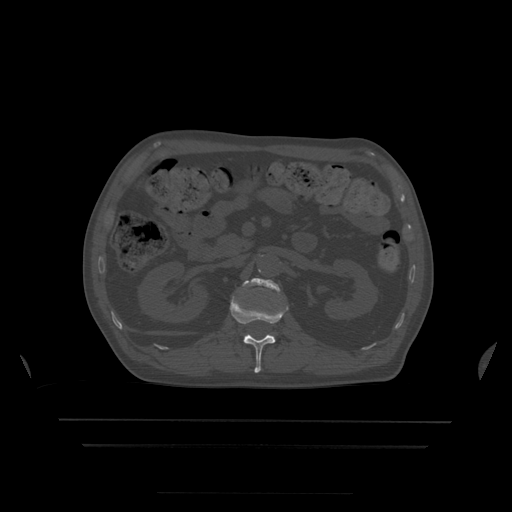
CT including the spine, one axial slice; position 164 of 522 along the scan axis; bone window (W 1800 / L 400 HU); 1.25 mm slice thickness; 512 × 512 image matrix, field of view 436 × 436 mm. Patient age 68 years. From the clinical record (not read from this slice): primary cancer: urothelial.
Outlined on this slice (semi-automatically segmented with operator editing):
- L1 vertebra: bounding box (x1, y1, x2, y2) in pixels: (230, 297, 288, 373)
- L2 vertebra: (243, 278, 281, 293)